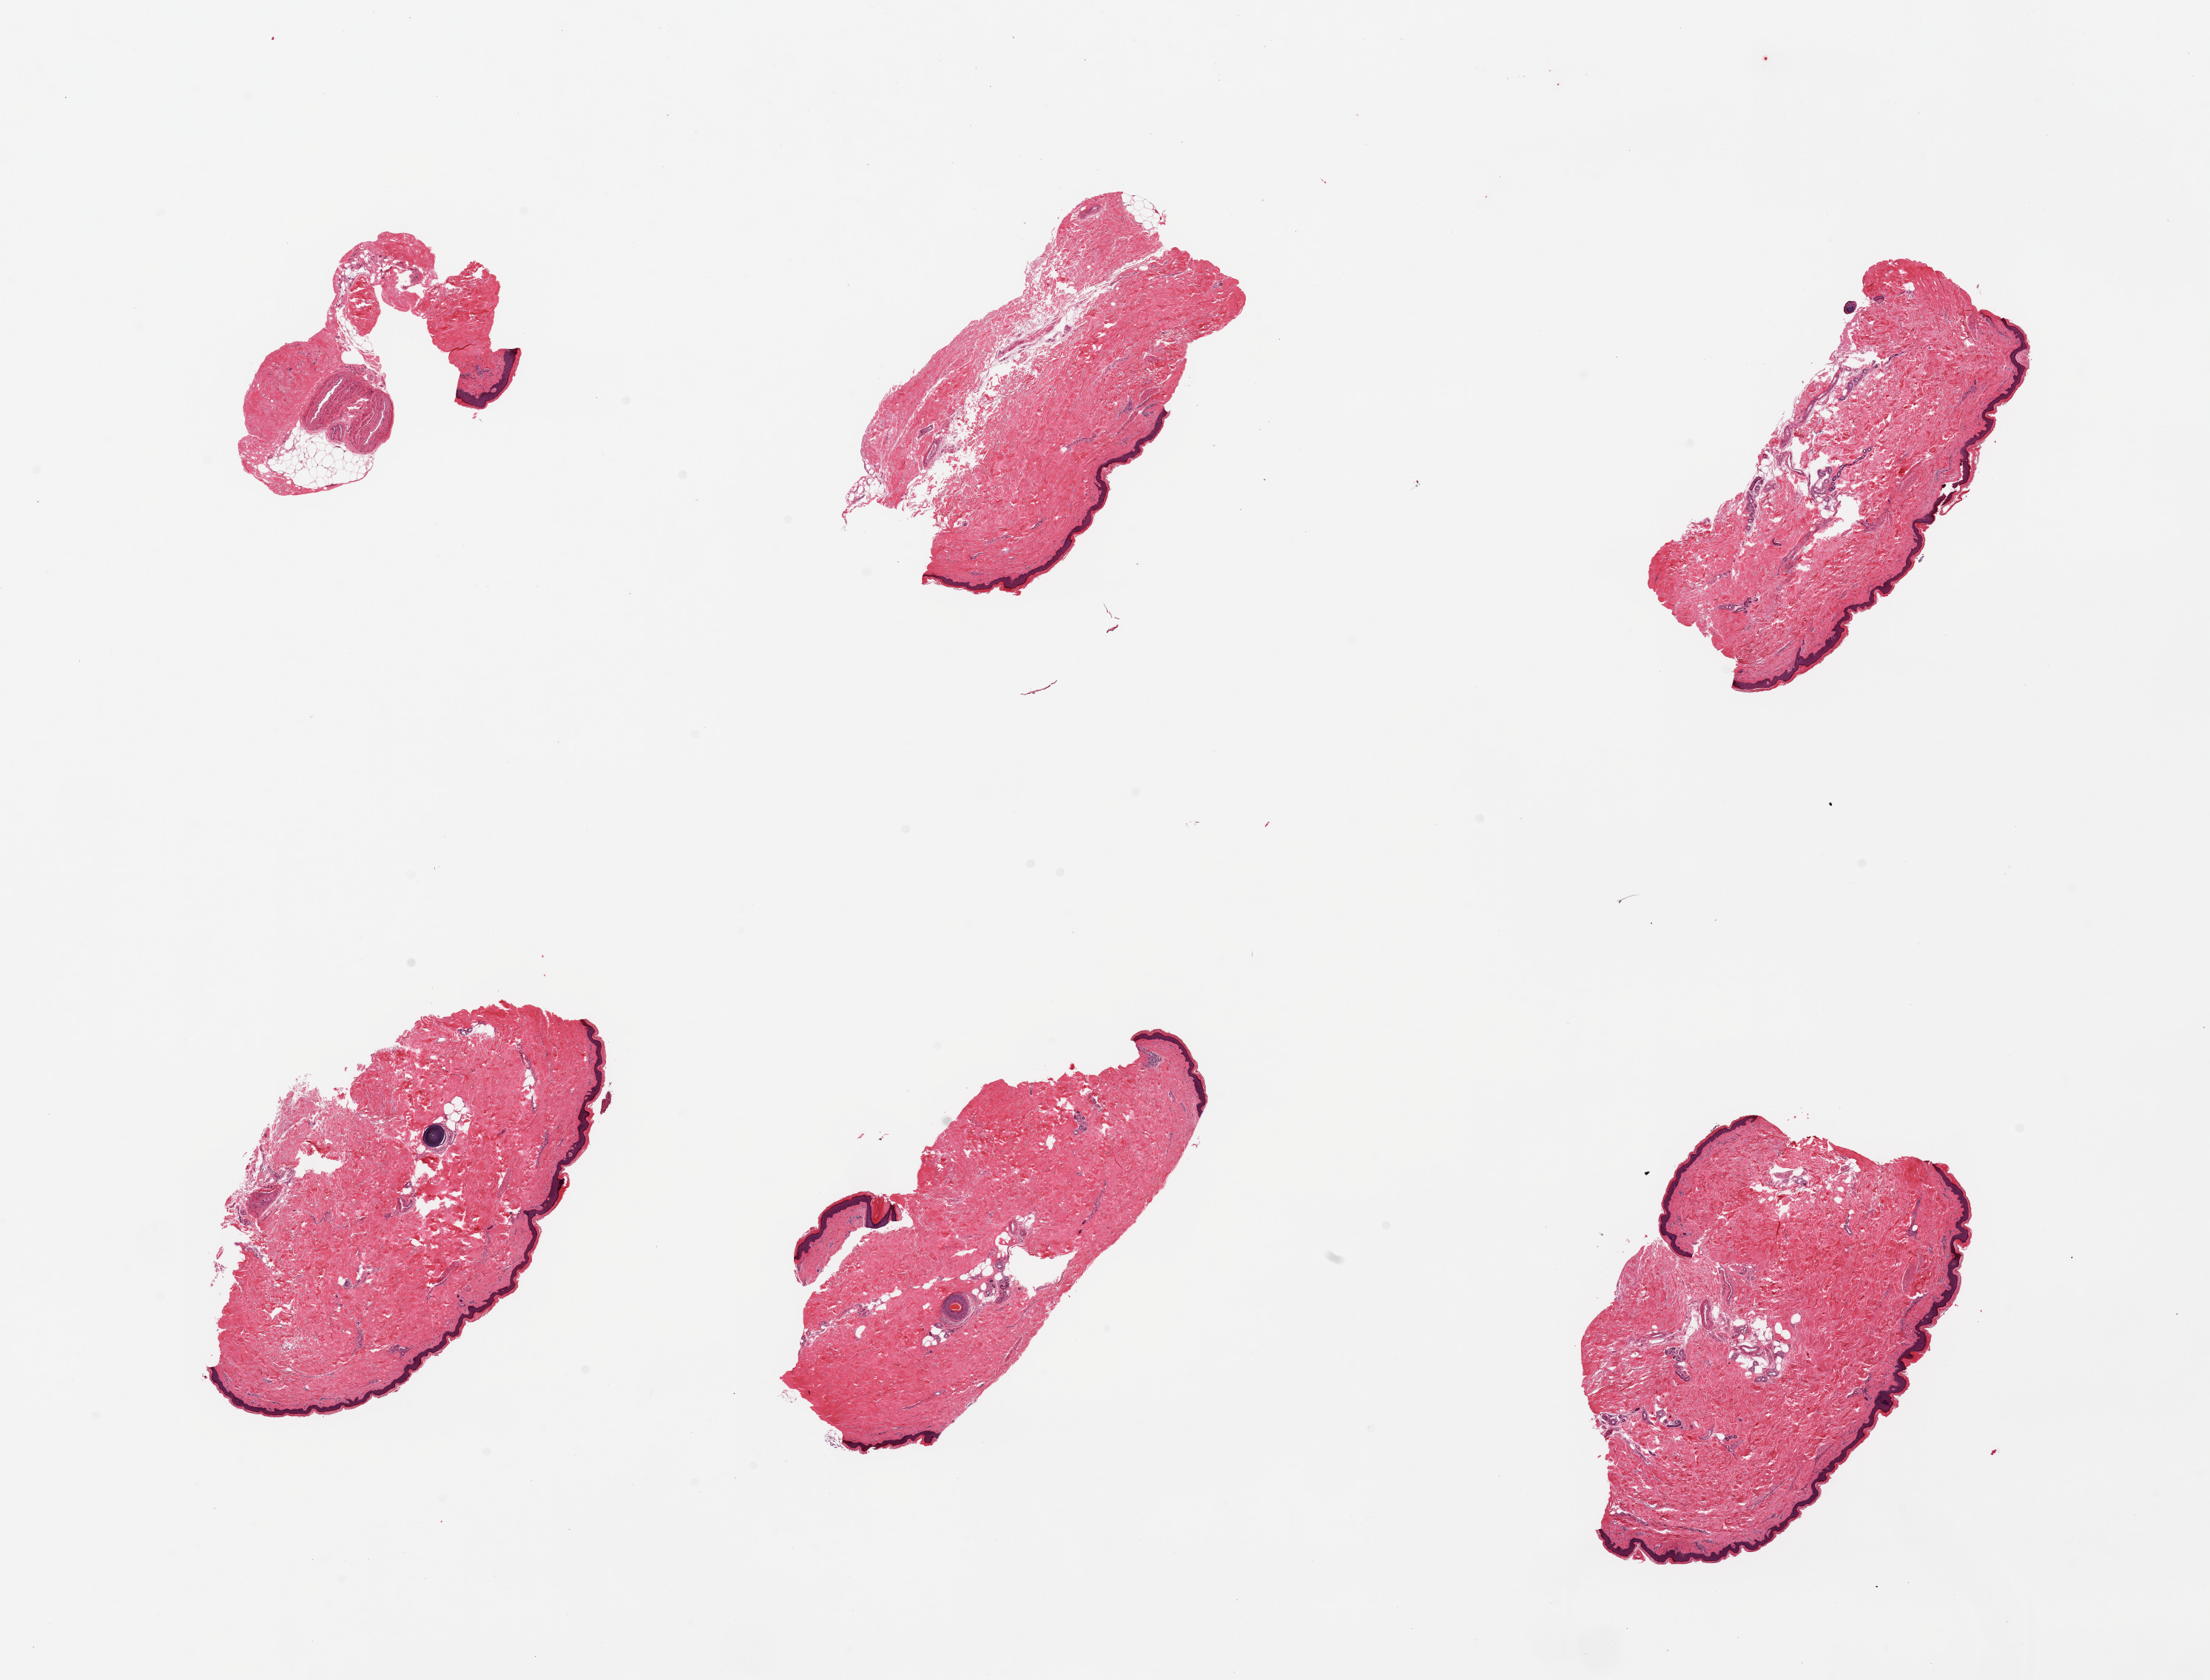
Hematoxylin and eosin (H&E) whole-slide image, brightfield, low-resolution overview of the scanned area, about 23.6 x 18.0 mm, PAXgene-fixed, paraffin-embedded tissue, target tissue: skin of lower leg, tissue donor sample. Donor sex: male.
Reviewer comment on this tissue sample: 6 pieces; ~10% internal fat (periadnexal); epidermis ~40 um thick.